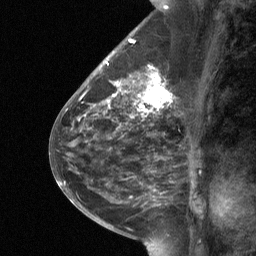
Breast MRI (dynamic contrast-enhanced), one sagittal slice. Position 27 of 64 along the scan axis. Dynamic contrast-enhanced study with each time point stored as its own series, time point 2 of 3 at this slice position (early post-contrast, ordered by acquisition time). 1.5 T. TE 4.8 ms, TR 27 ms. 256 × 256 image matrix. Patient: female, 59 years. From the clinical record (not read from this slice): setting: breast cancer imaged before/during neoadjuvant chemotherapy; receptor status: triple-negative.
Structures marked on this image (semi-automatic segmentation, software-assisted and operator-edited):
- analysis volume of interest (the breast-tissue region the enhancement analysis was run in; not a lesion): bounding box (x1, y1, x2, y2) in pixels: (113, 66, 174, 120)
- tumour enhancement mask (voxels above the 90 % enhancement threshold inside the analysis volume of interest): (113, 67, 170, 112)